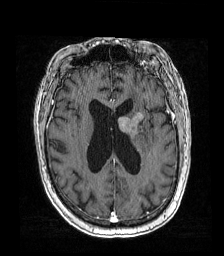
Brain MRI from a brain-tumour surgery series, one axial slice; slice 69 of 192 in the series (ordered by position); T1-weighted post-contrast; 224 × 256 image matrix, field of view 219 × 250 mm. Case-level facts recorded for this patient, not image findings: histopathology: Metastatic carcinoma from lung primary; tumour location: Left Frontal Caudate.
Annotated regions visible in this slice (manually delineated by an expert):
- tumour: bounding box (x1, y1, x2, y2) in pixels: (119, 111, 144, 136)